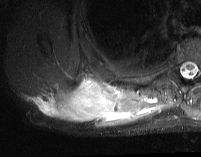
MRI of an extremity soft-tissue mass, one axial slice. Position 21 of 74 along the scan axis. STIR. MR volume resampled by the dataset authors to the PET/CT grid (not the native acquisition matrix). 3.27 mm slice thickness. 201 × 157 image matrix. Male patient. From the clinical record (not read from this slice): histological type: pleiomorphic spindle cell undifferentiated; grade: high; site of the primary tumour: right parascapusular.
Annotated regions visible in this slice (expert contour drawn on MRI and transferred to this co-registered scan by the dataset authors):
- gross tumour volume including surrounding oedema: bounding box [x1, y1, x2, y2] px = [30, 77, 161, 129]
- gross tumour volume (mass): [46, 80, 118, 122]